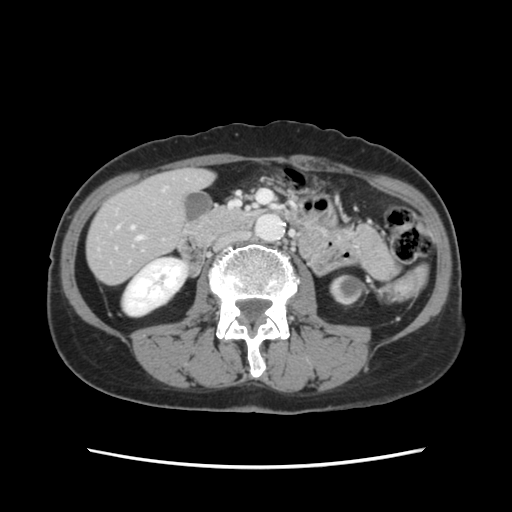
Contrast-enhanced abdominal CT, one axial slice; position 28 of 120 along the scan axis; 120 kVp; intravenous contrast given; soft-tissue window (W 400 / L 40 HU); 2.5 mm slice thickness; 512 × 512 image matrix. Female patient, age 70 years. Case-level facts recorded for this patient, not image findings: diagnosis: colorectal cancer liver metastases, imaged before liver resection; multiple liver metastases: no; largest metastasis: 2.5 cm.
Outlined on this slice (manually delineated by an expert):
- hepatic veins: box from (x=137, y=236) to (x=142, y=240) px
- liver: (x=88, y=171)–(x=210, y=283)
- planned liver remnant (the part of the liver to remain after resection): (x=88, y=171)–(x=209, y=283)
- portal vein (with intrahepatic branches): (x=131, y=226)–(x=135, y=230)